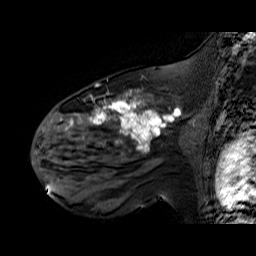
Breast MRI (dynamic contrast-enhanced), one sagittal slice; slice 39 of 60 in the series (ordered by position); dynamic contrast-enhanced series, time point 2 of 6 at this slice position (early post-contrast); 1.5 T; TE 6.3 ms, TR 32.9 ms; 4 mm slice thickness; 256 × 256 image matrix, field of view 200 × 200 mm. Female patient. Case-level facts recorded for this patient, not image findings: setting: breast cancer imaged before/during neoadjuvant chemotherapy; receptor status: HER2-positive.
Outlined on this slice (semi-automatic segmentation, software-assisted and operator-edited):
- analysis volume of interest (the breast-tissue region the enhancement analysis was run in; not a lesion): bounding box [x1, y1, x2, y2] px = [48, 92, 195, 174]
- tumour enhancement mask (voxels above the 100 % enhancement threshold inside the analysis volume of interest): [61, 92, 177, 149]